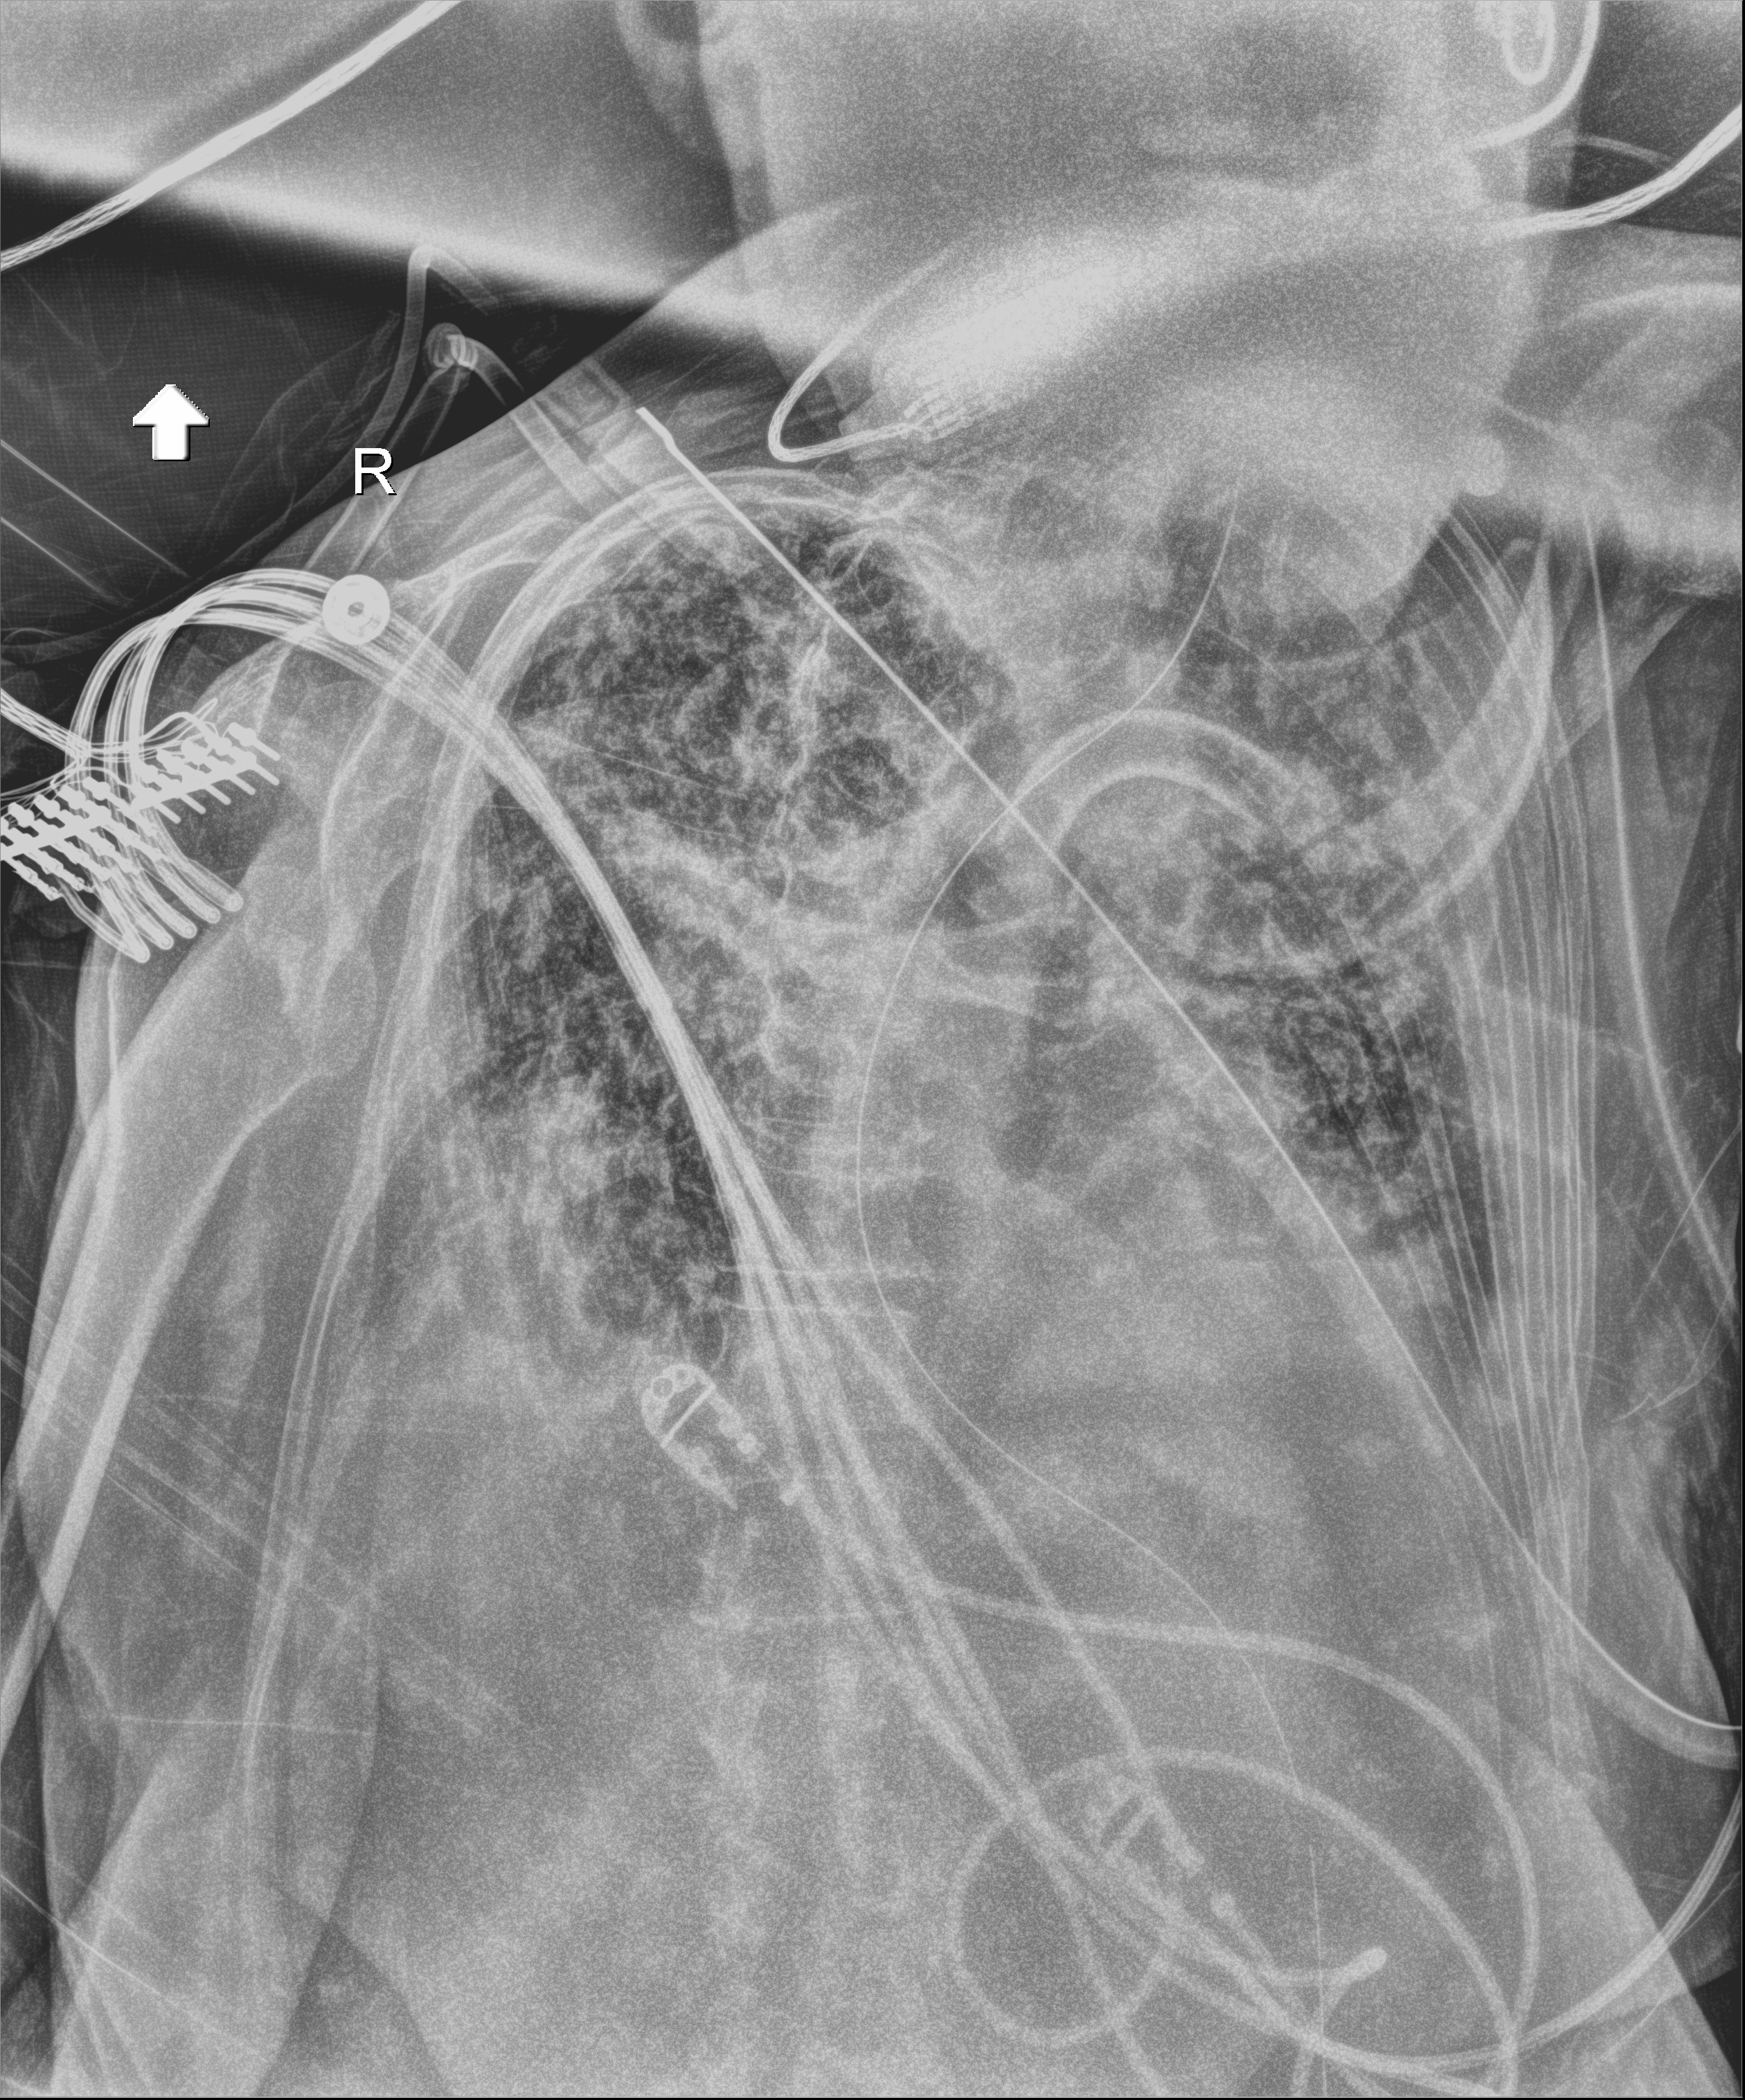
Chest X-ray (portable); anteroposterior (AP) projection. Female patient hospitalised with COVID-19, age 75–90 years.
Admission-level facts for this patient (not findings on this image; timing relative to this image not recorded): admitted to intensive care during this hospital stay: yes; mechanically ventilated during this hospital stay: yes.